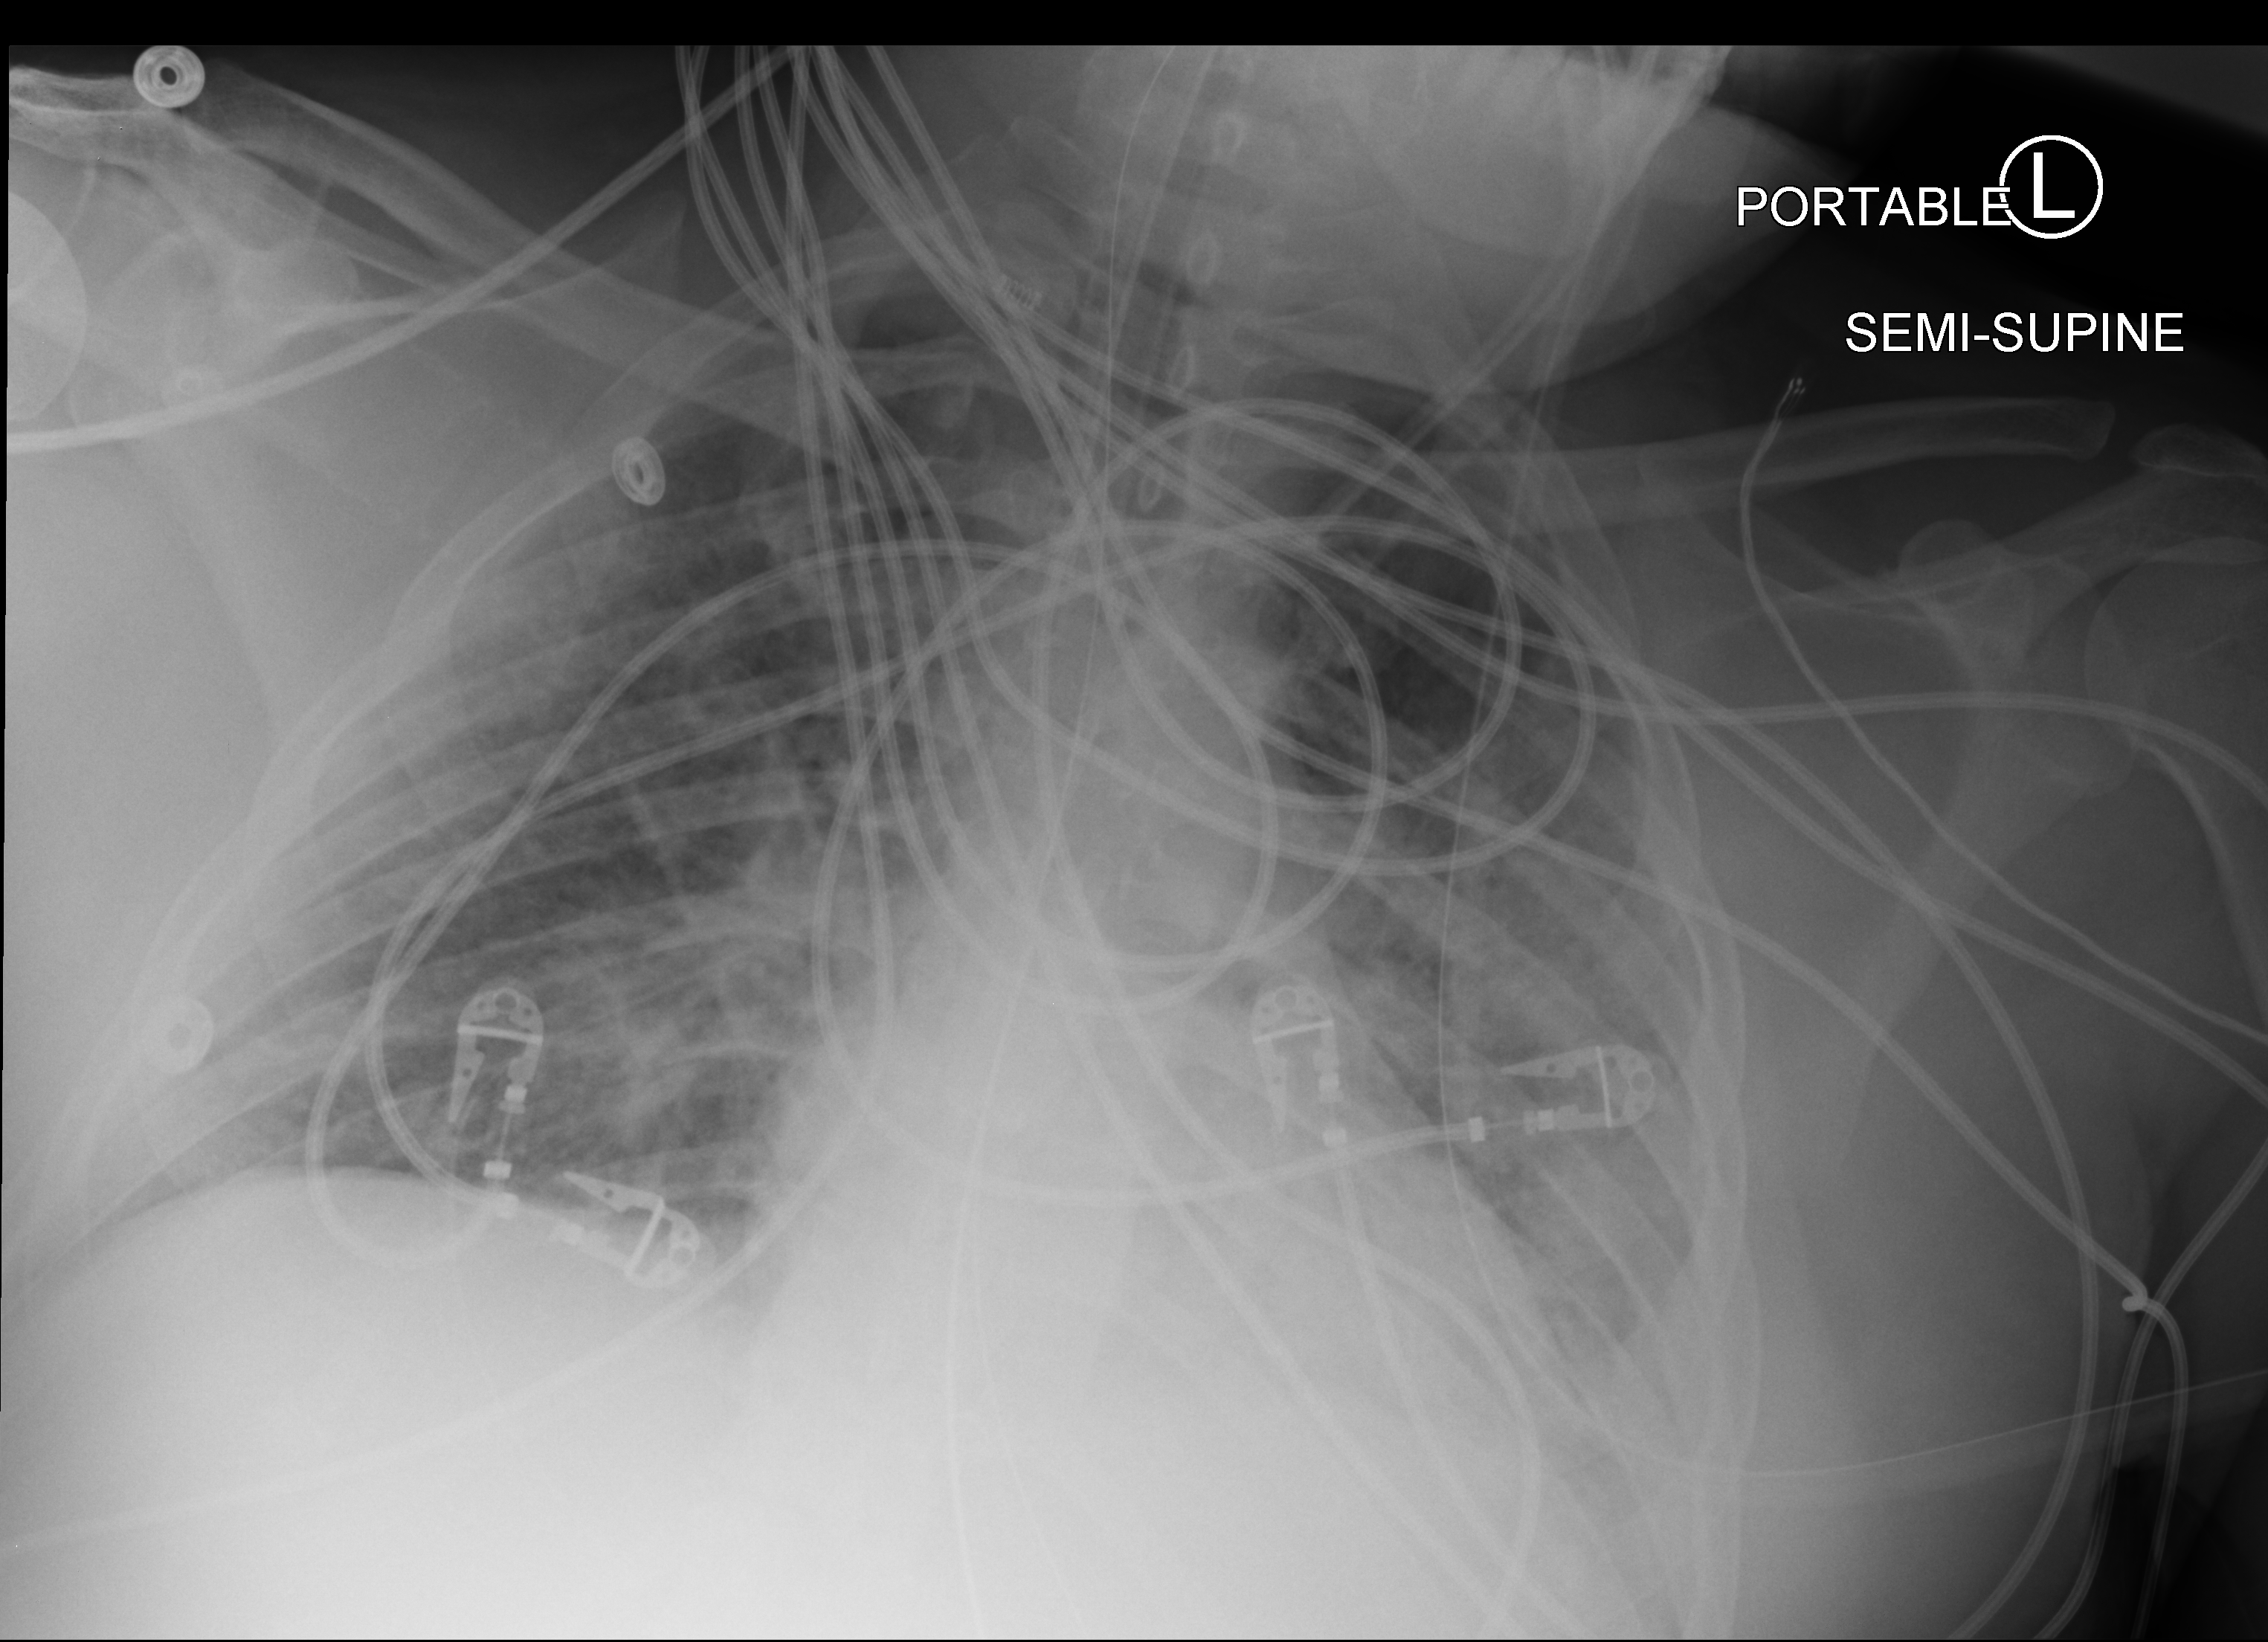
Chest X-ray (portable), anteroposterior (AP) projection. Adult patient hospitalised with COVID-19, age 18–59 years.
Hospital-stay facts (about this admission, not read from this image; timing relative to this image not recorded): mechanically ventilated during this hospital stay: yes; other chronic lung disease (admission record): no.